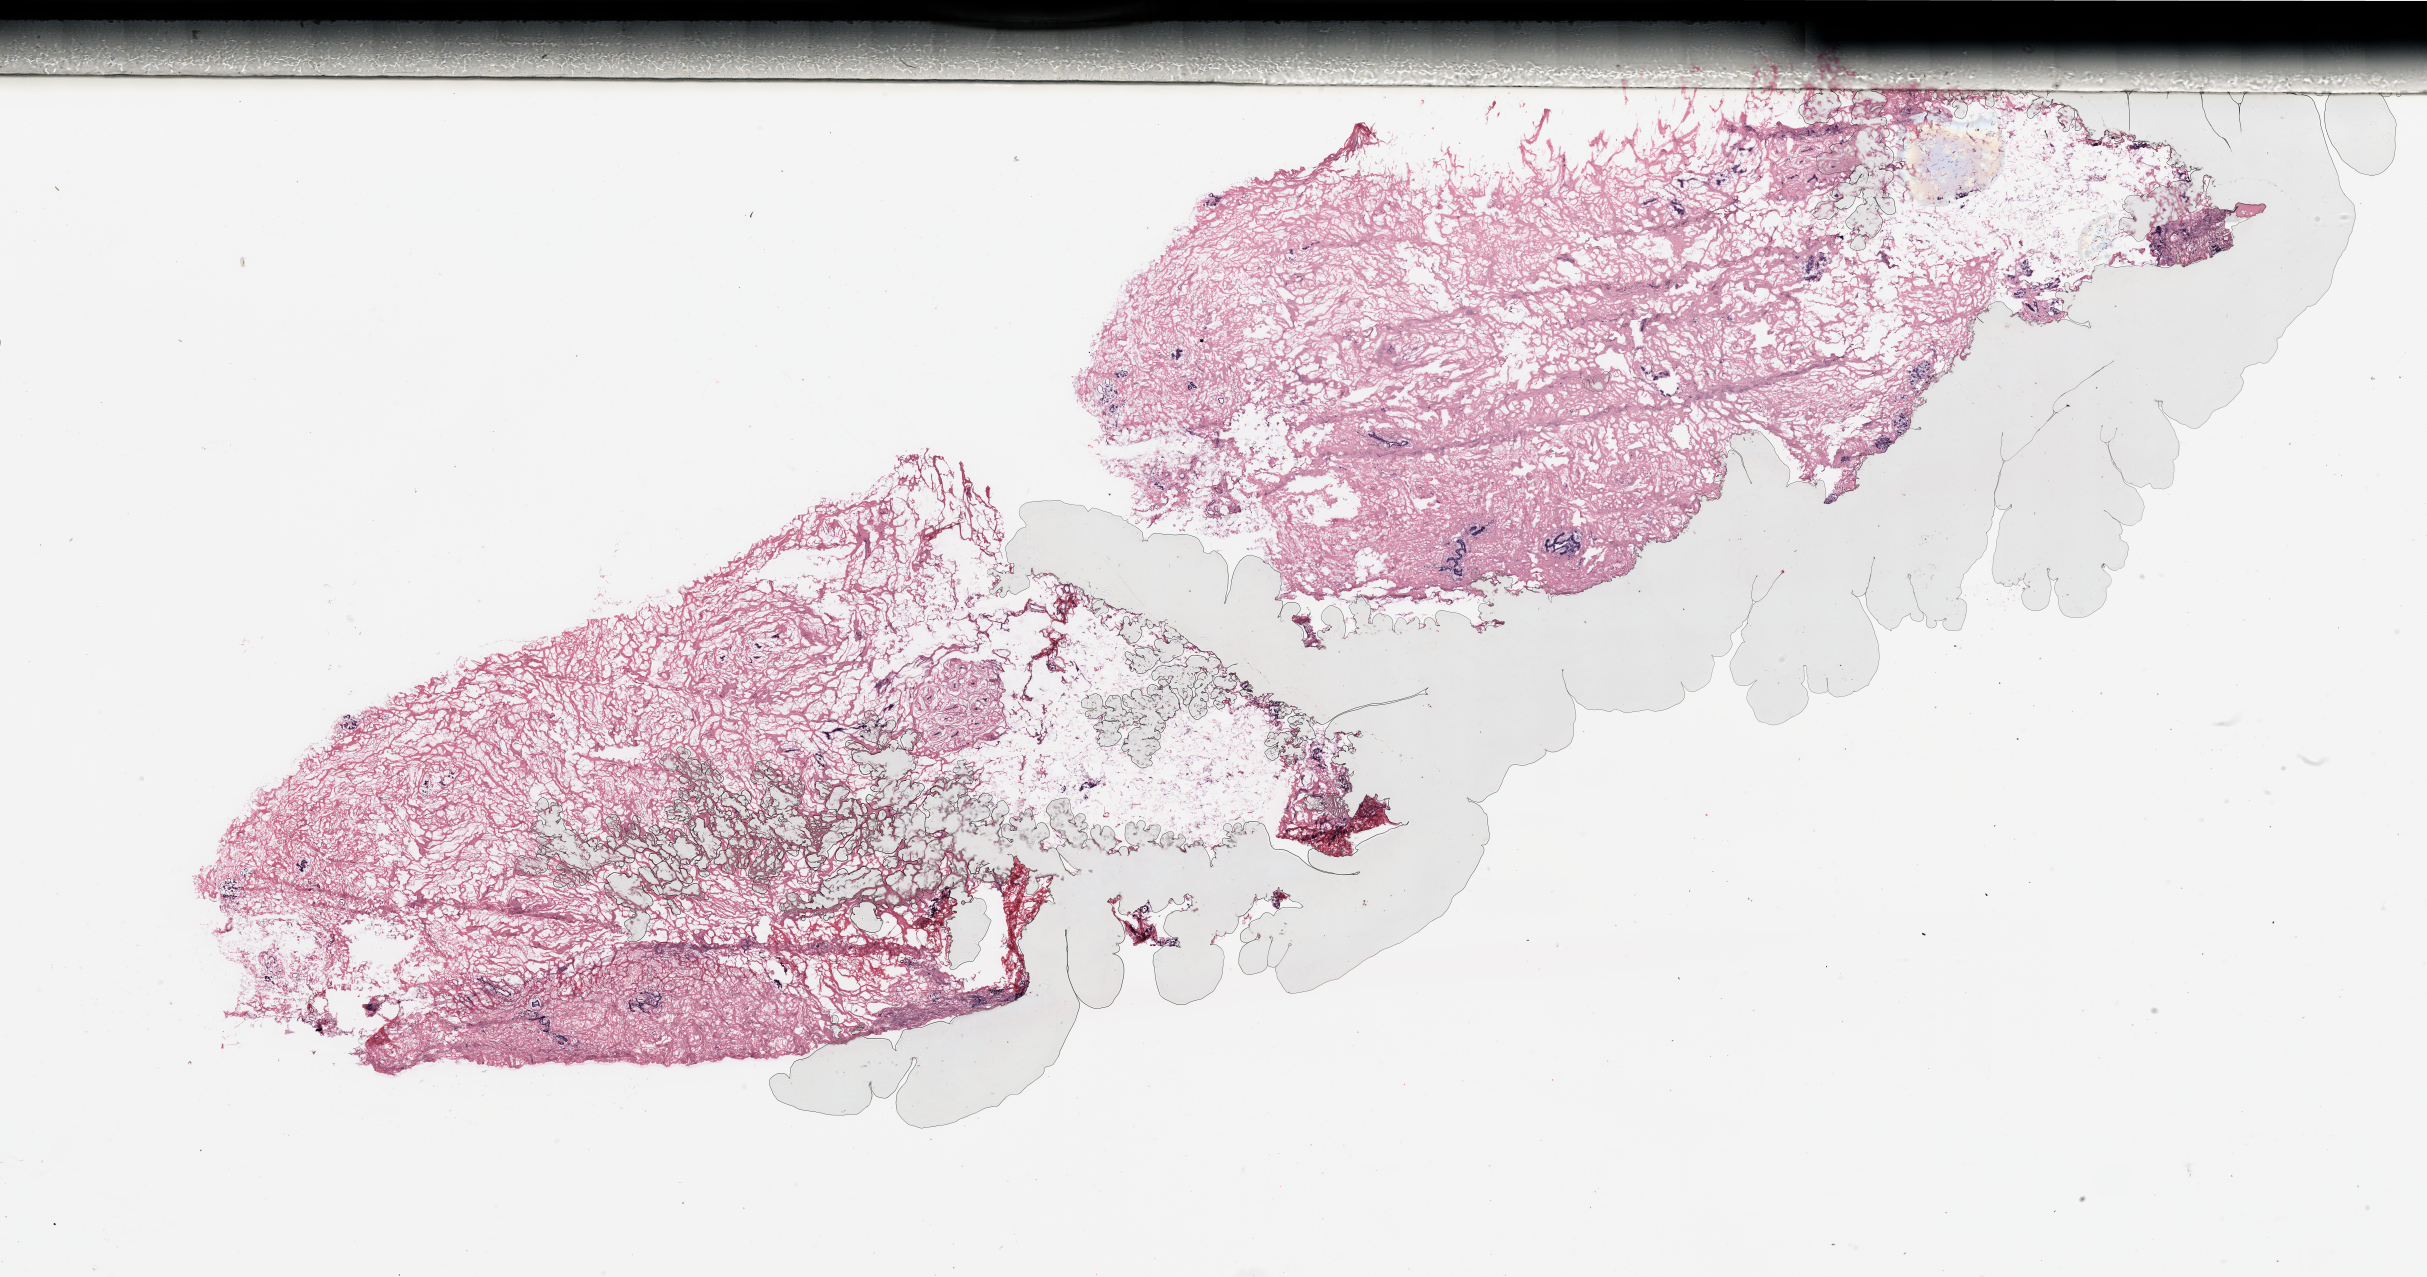
Digitized H&E-stained tissue section (whole slide) — low-resolution overview of the scanned area, about 38.4 x 20.2 mm (slide scanned at 20x), tumour tissue sample, breast. Patient: female, age 50 years.
* AJCC pathologic stage: IIA
* histologic diagnosis: Infiltrating duct carcinoma, NOS